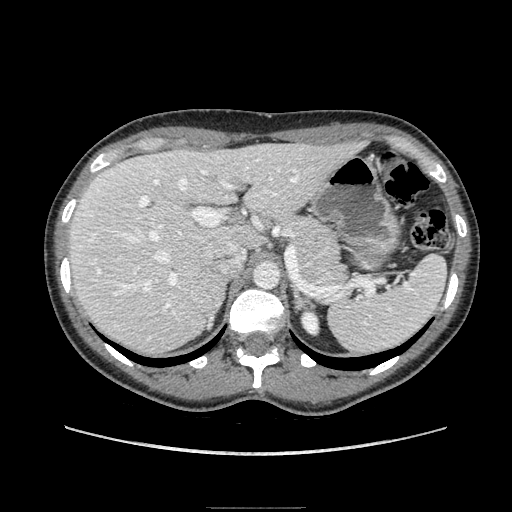
Contrast-enhanced abdominal CT, one axial slice; position 124 of 193 along the scan axis; soft-tissue window (W 400 / L 40 HU); 1.25 mm slice thickness; 512 × 512 image matrix. Female patient. Case-level facts recorded for this patient, not image findings: diagnosis: adrenocortical carcinoma; tumour side: right adrenal; tumour size at pathology: 3 cm; Ki-67 index: 4 %; stage (as recorded): 1.
Structures marked on this image (semi-automatic segmentation, software-assisted and operator-edited):
- mass: bounding box (x1, y1, x2, y2) in pixels: (192, 271, 226, 326)